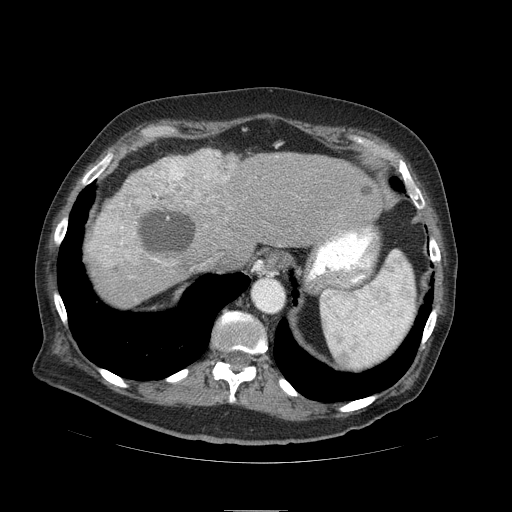
Contrast-enhanced abdominal CT (liver protocol), one axial slice. Position 74 of 103 along the scan axis. Reconstruction kernel STANDARD. 120 kVp. Soft-tissue window (W 400 / L 40 HU). 2.5 mm slice thickness. 512 × 512 image matrix. From the clinical record (not read from this slice): diagnosis: hepatocellular carcinoma (patient treated with transarterial chemoembolisation; whether this scan precedes or follows treatment is not stated here); TNM stage (as recorded): Stage-IIIA; Child-Pugh class: B.
Structures marked on this image (semi-automatic segmentation, software-assisted and operator-edited):
- liver parenchyma outside the tumour (the mass and vessels are separate outlines, so this box may not span the whole liver): bounding box (x1, y1, x2, y2) in pixels: (86, 148, 390, 306)
- mass: (90, 152, 246, 262)